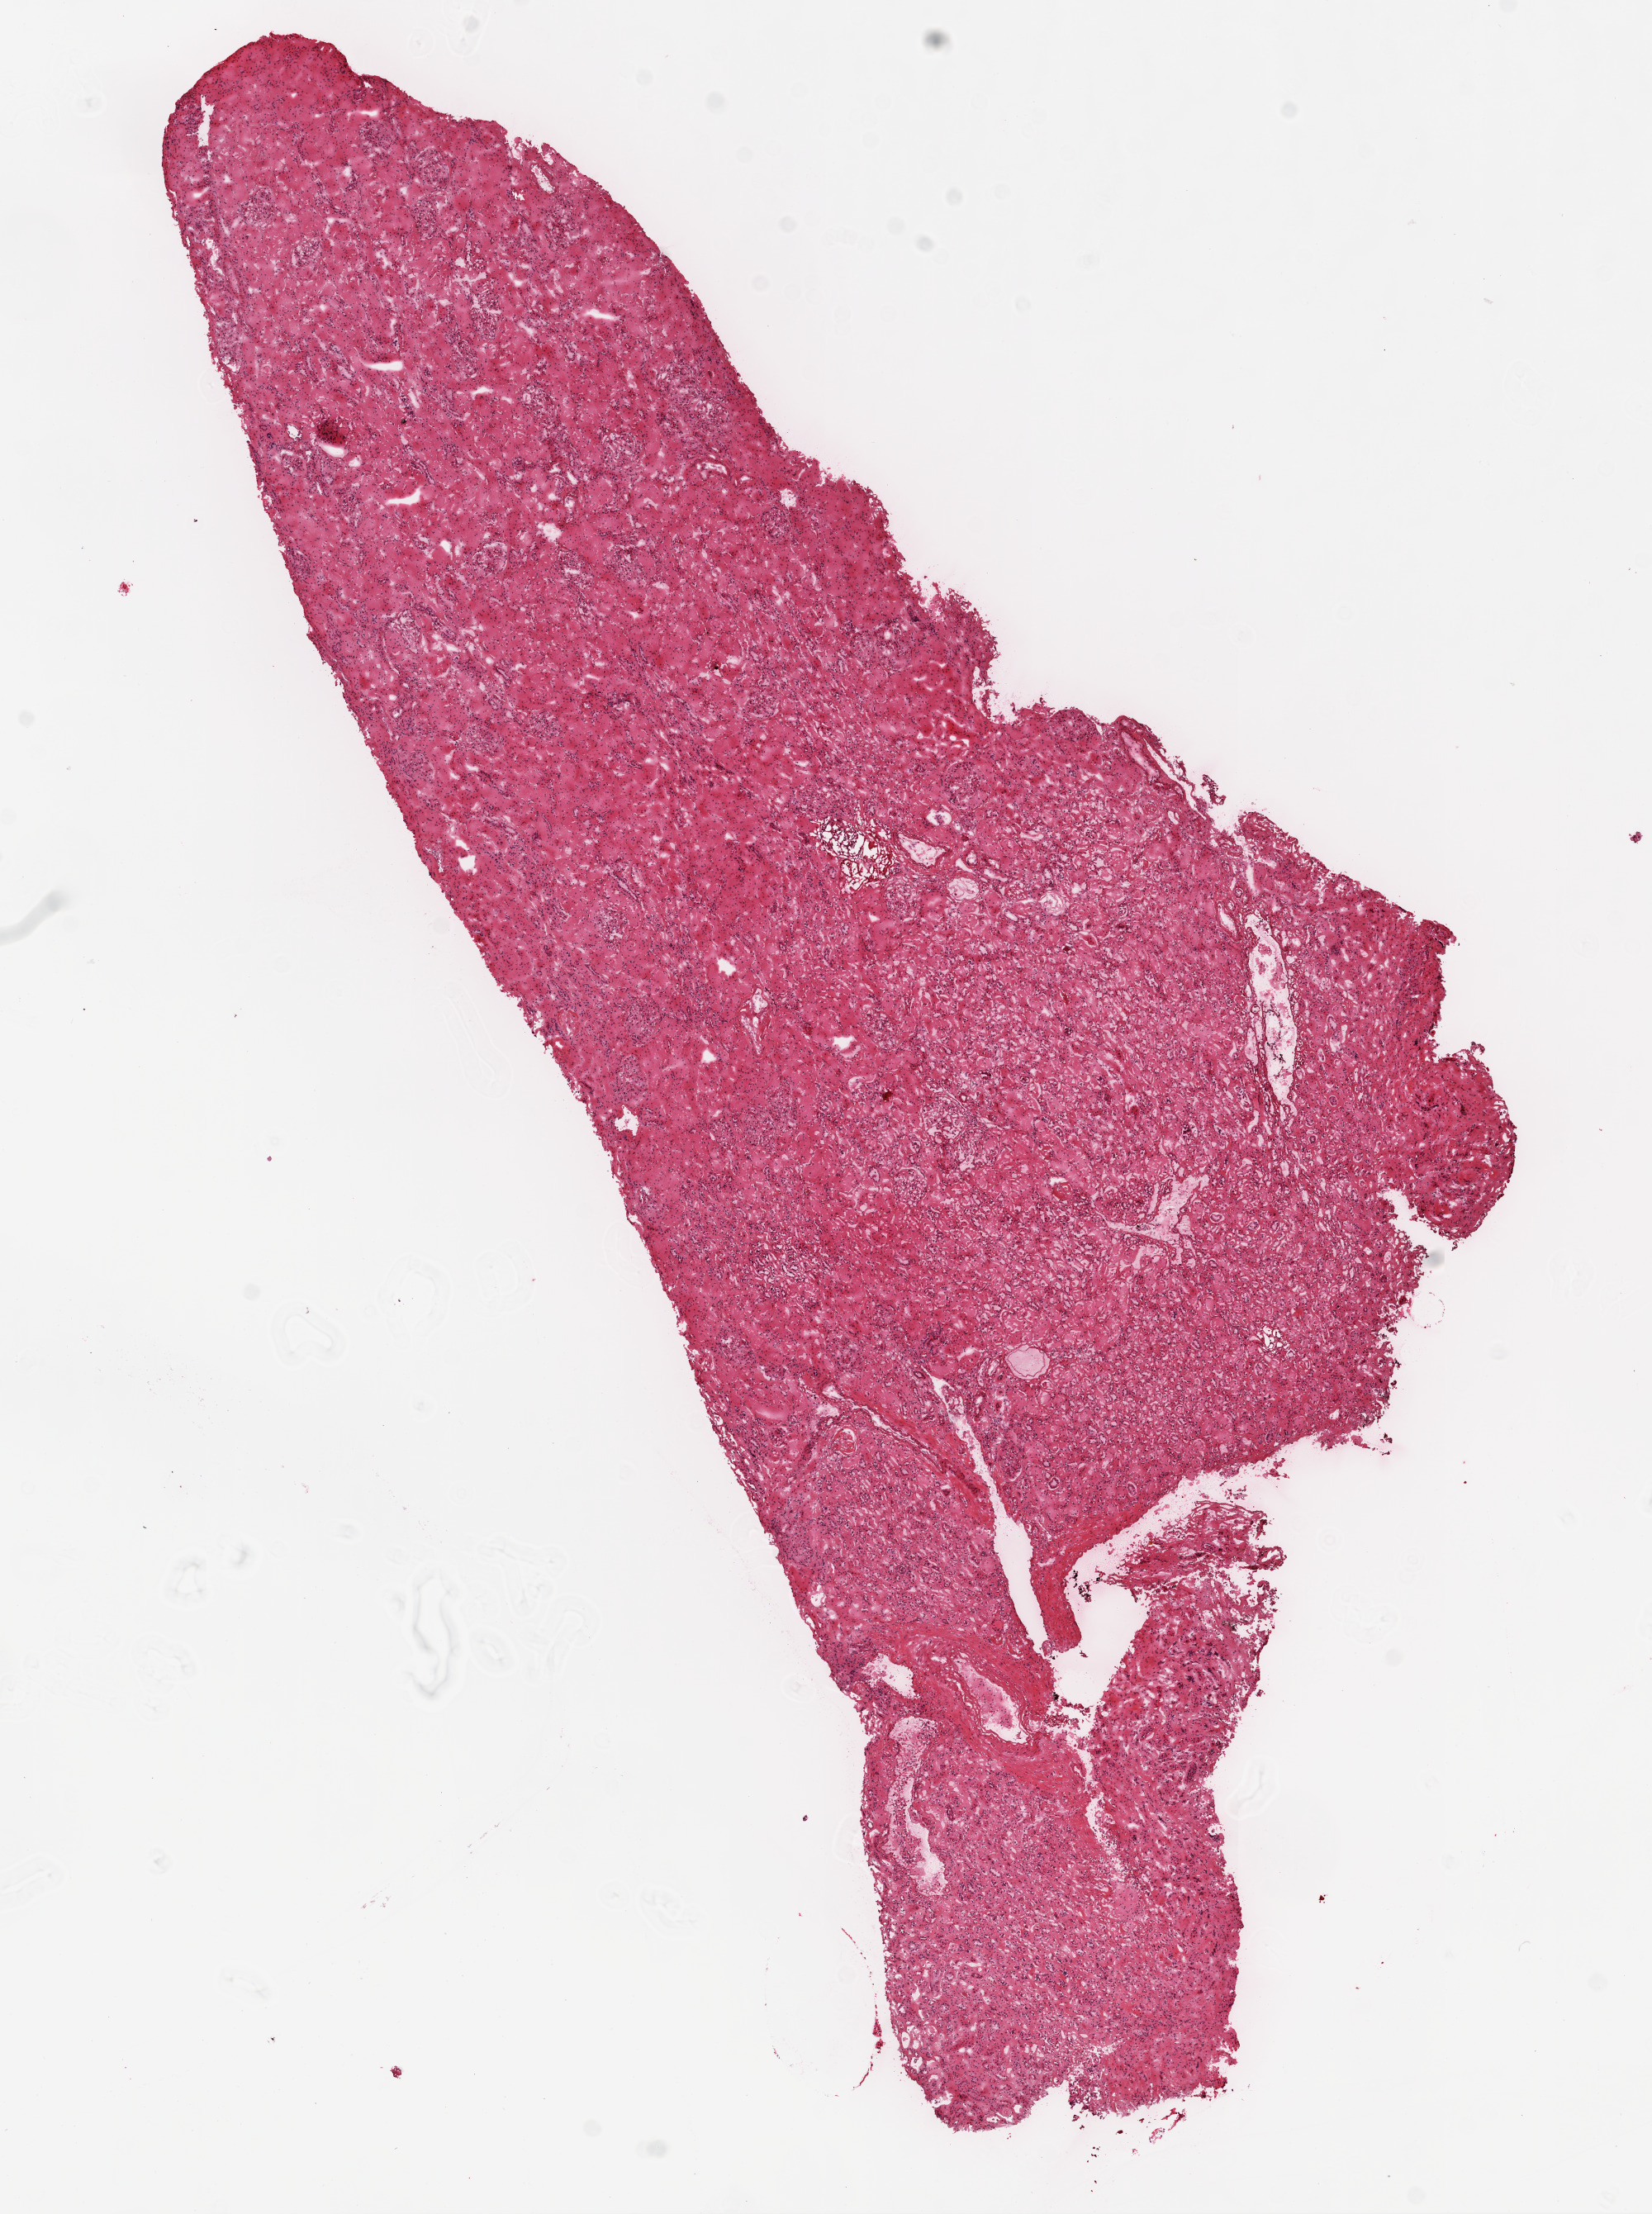
Digitized H&E-stained tissue section (whole slide) — whole scanned area (about 8.0 x 10.8 mm, acquisition: 20x scan) shown as a low-resolution overview, frozen section from the top of the tissue portion, sample: solid tissue normal (non-tumour tissue), kidney. Male patient; age at initial diagnosis 59 years.
This section: solid tissue normal sample (biorepository sample class). Patient diagnosis: Clear cell adenocarcinoma, NOS.